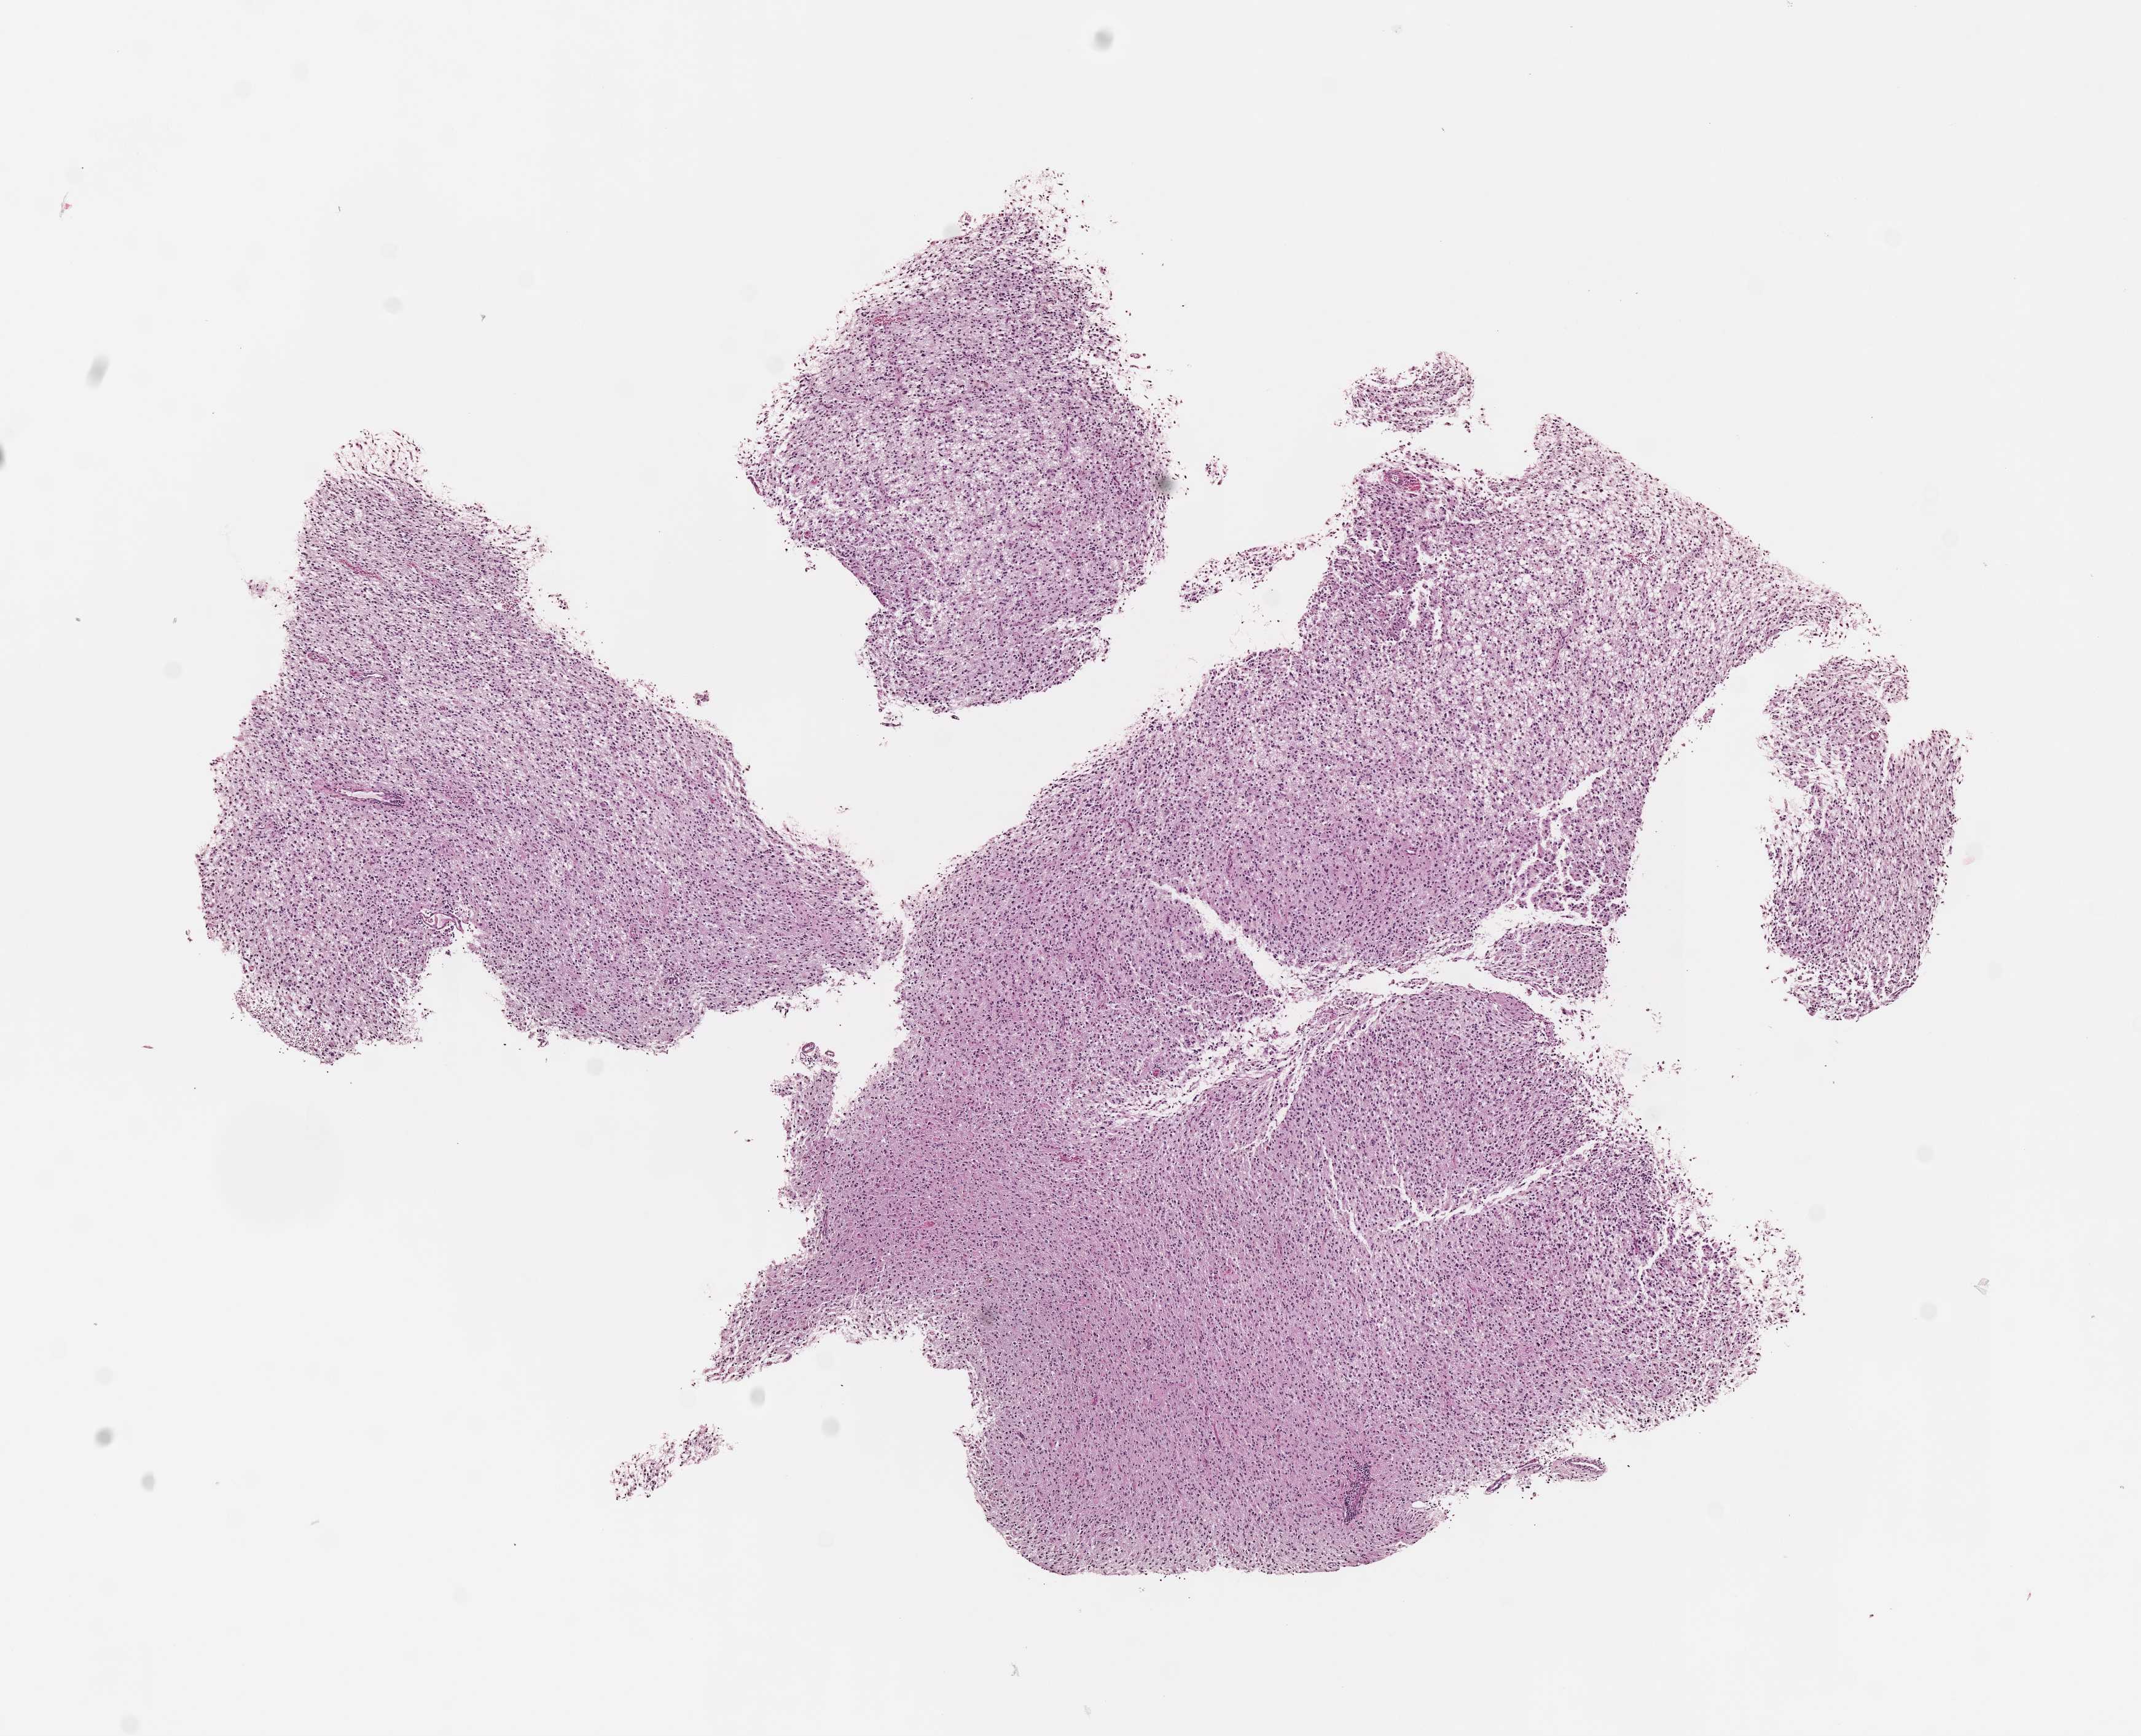
H&E whole-slide image — shown as a low-resolution overview of the whole scanned area (about 7.0 x 5.7 mm); formalin-fixed paraffin-embedded (FFPE) diagnostic section; sample: primary tumour, brain. Male patient; age at initial diagnosis 51 years. Histologic grade: G2 (moderately differentiated).
Diagnosis: Mixed glioma (cerebrum).